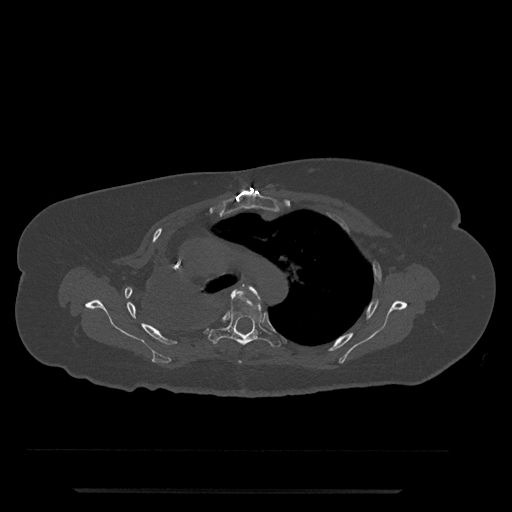
CT including the spine, one axial slice; position 552 of 797 along the scan axis; reconstruction kernel Br40s/3; 120 kVp; bone window (W 1800 / L 400 HU); 512 × 512 image matrix, field of view 440 × 440 mm. Patient: female, 51 years. From the clinical record (not read from this slice): primary cancer: neuro.
Annotated regions visible in this slice (semi-automatically segmented with operator editing):
- T4 vertebra: bounding box (x1, y1, x2, y2) in pixels: (238, 286, 260, 363)
- T5 vertebra: (208, 289, 281, 347)